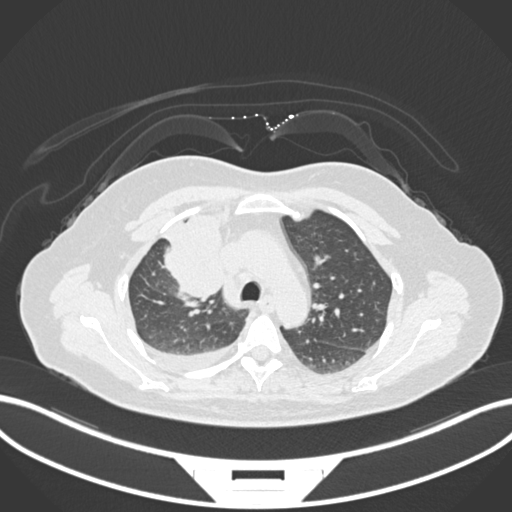
Chest CT, one axial slice. Slice 112 of 172 in the series (ordered by position). Lung window (W 1500 / L -600 HU). 1 mm slice thickness. 512 × 512 image matrix, field of view 400 × 400 mm. Patient: female, 52 years. From the clinical record (not read from this slice): clinical TNM (as recorded): T3 N1 M1.
Outlined on this slice (bounding box drawn by a radiologist):
- lung tumour (recorded histology: adenocarcinoma): box from (x=153, y=203) to (x=230, y=303) px